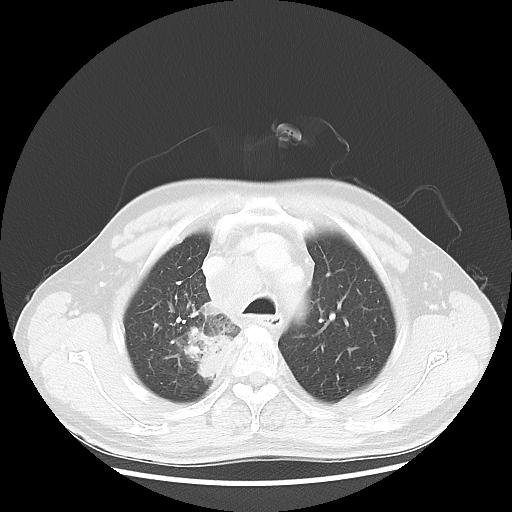
Chest CT, one axial slice; slice 45 of 60 in the series (ordered by position); 100 kVp; lung window (W 1500 / L -600 HU); 512 × 512 image matrix, field of view 382 × 382 mm. Male patient, age 64 years. From the clinical record (not read from this slice): clinical TNM (as recorded): T3 N3 M0; histopathological grade: G3.
Outlined on this slice (rectangle marked by the reading radiologist):
- lung tumour (recorded histology: small cell carcinoma): bounding box <186,298,239,387> (left, top, right, bottom; pixels)